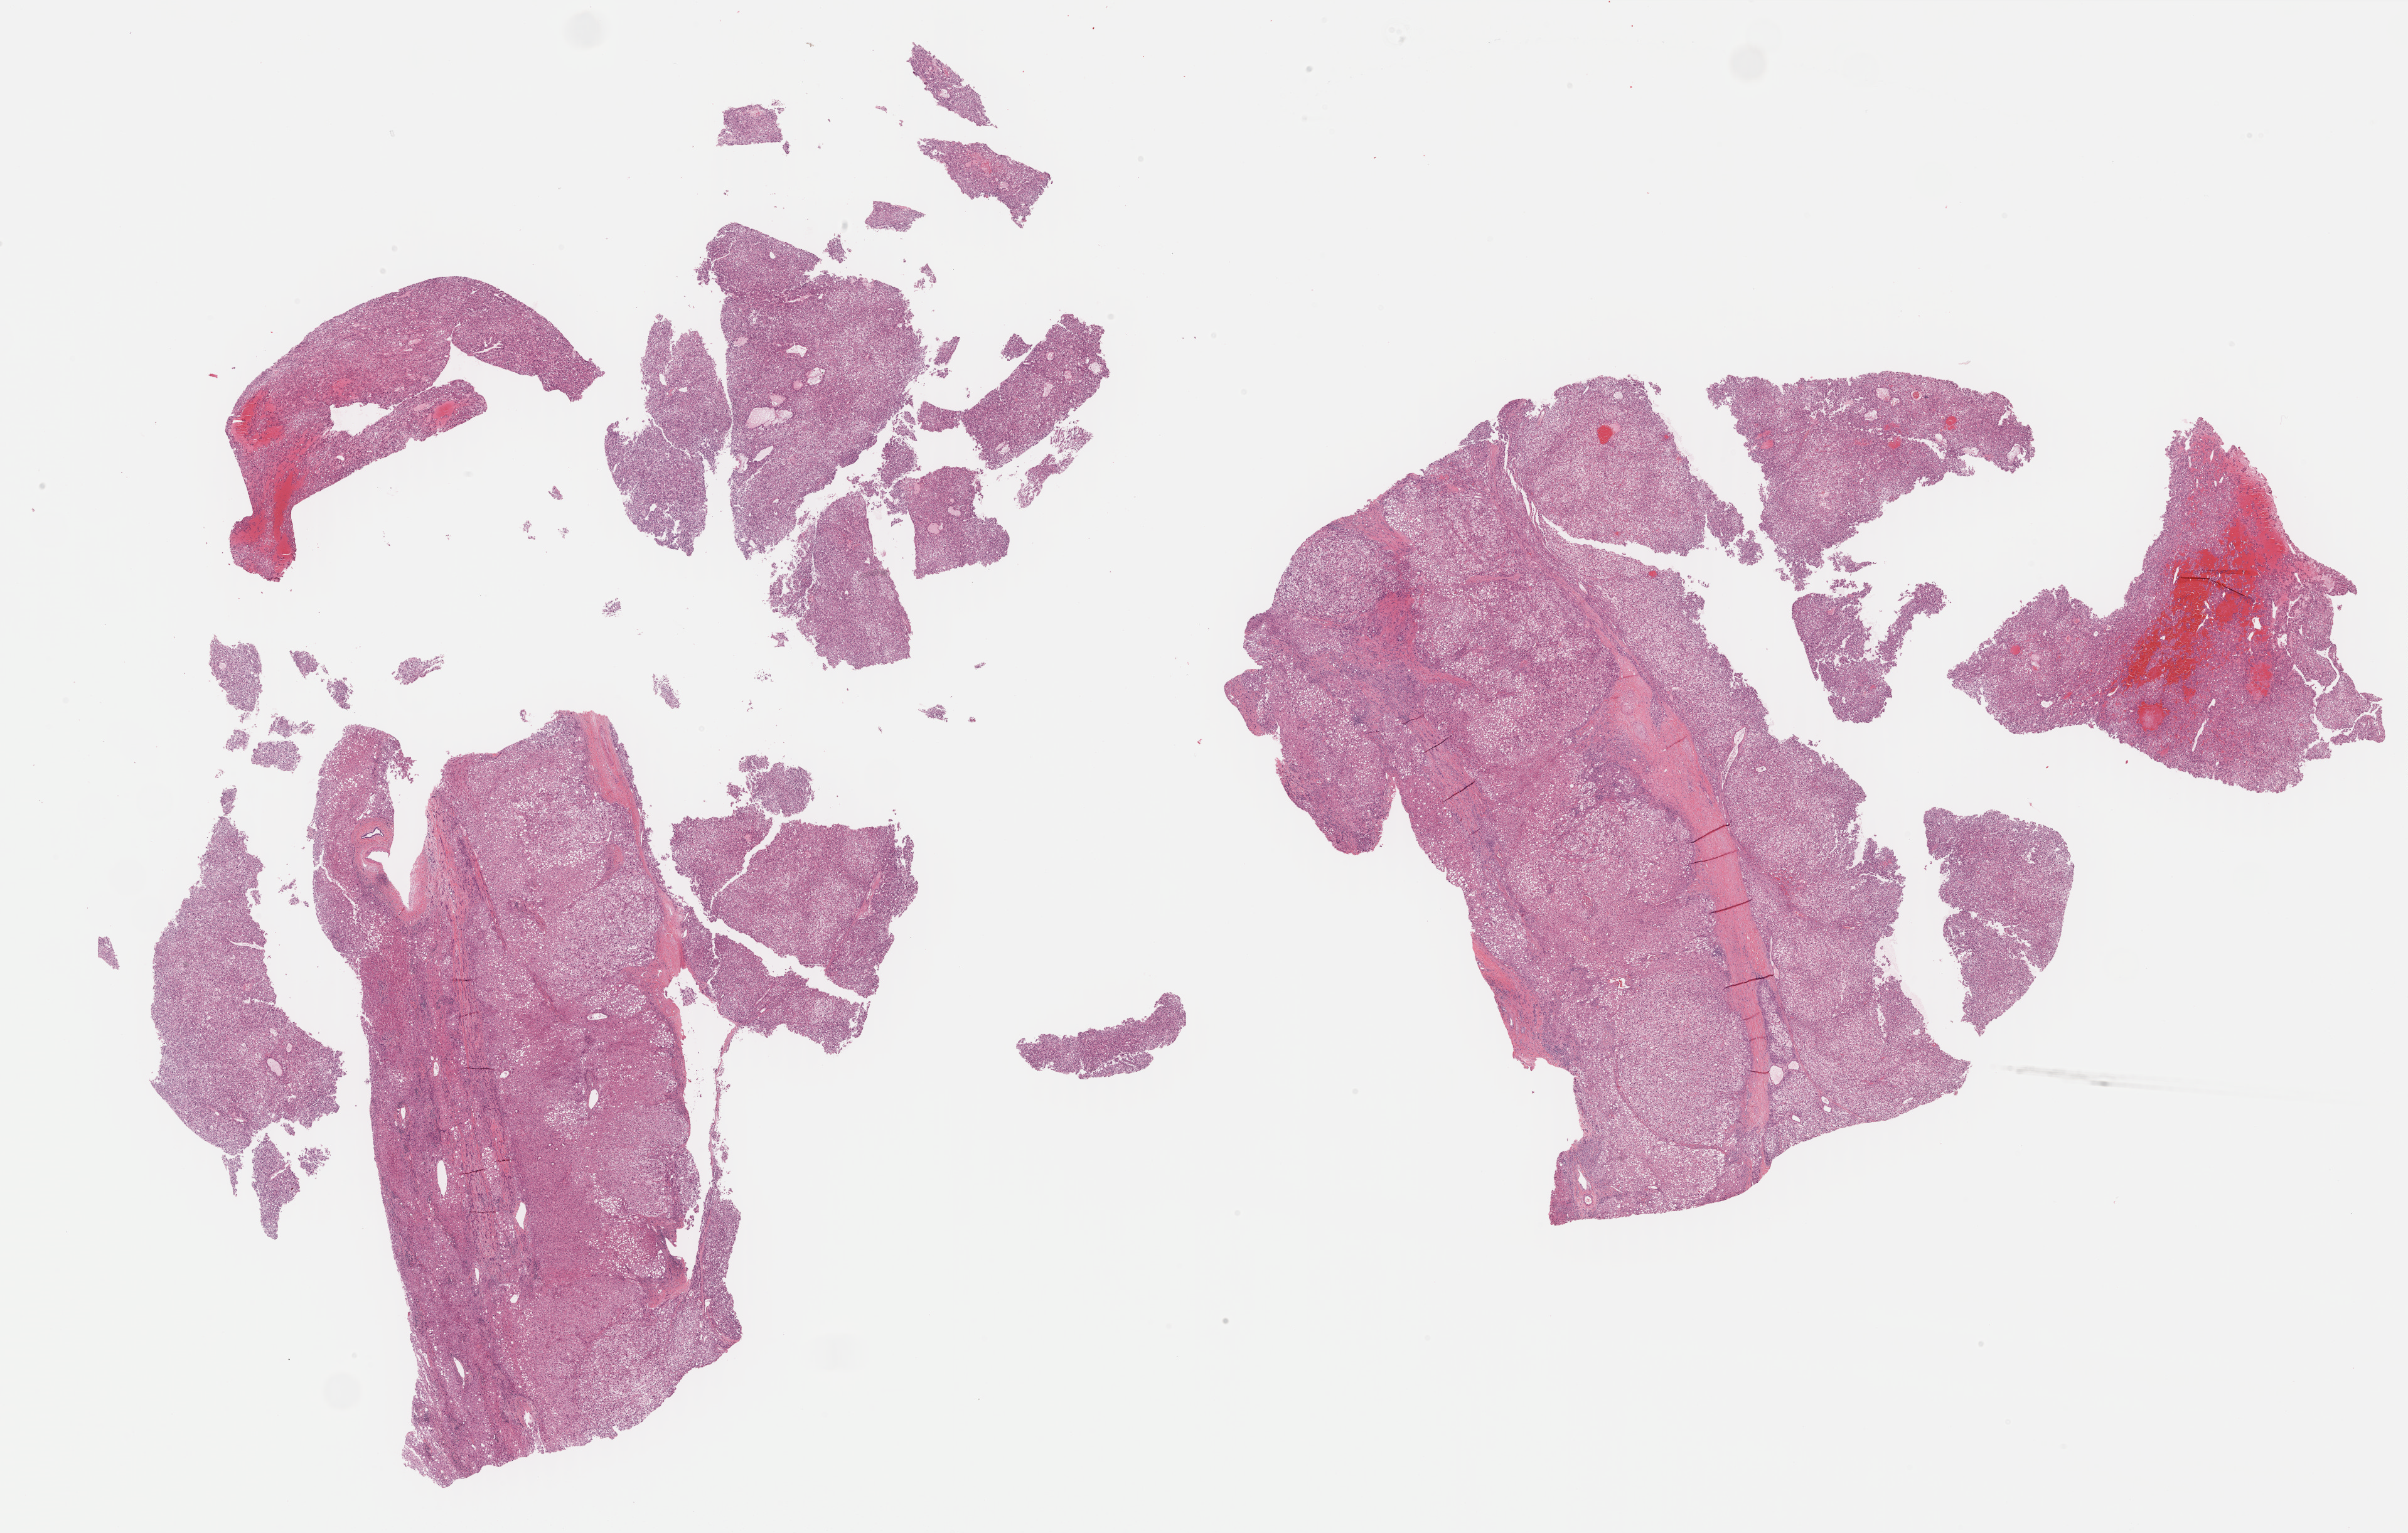
Hematoxylin and eosin (H&E) stained whole-slide image — low-resolution overview of the scanned area, about 31.1 x 19.8 mm (acquisition: 40x scan), formalin-fixed paraffin-embedded (FFPE) diagnostic section, liver, primary tumour sample. Patient: male, age at initial diagnosis 61 years. Histologic grade: G1 (well differentiated).
AJCC pathologic stage: IIIA (6th edition). Pathologic diagnosis: Hepatocellular carcinoma, NOS. TNM: T3 N0 M0.